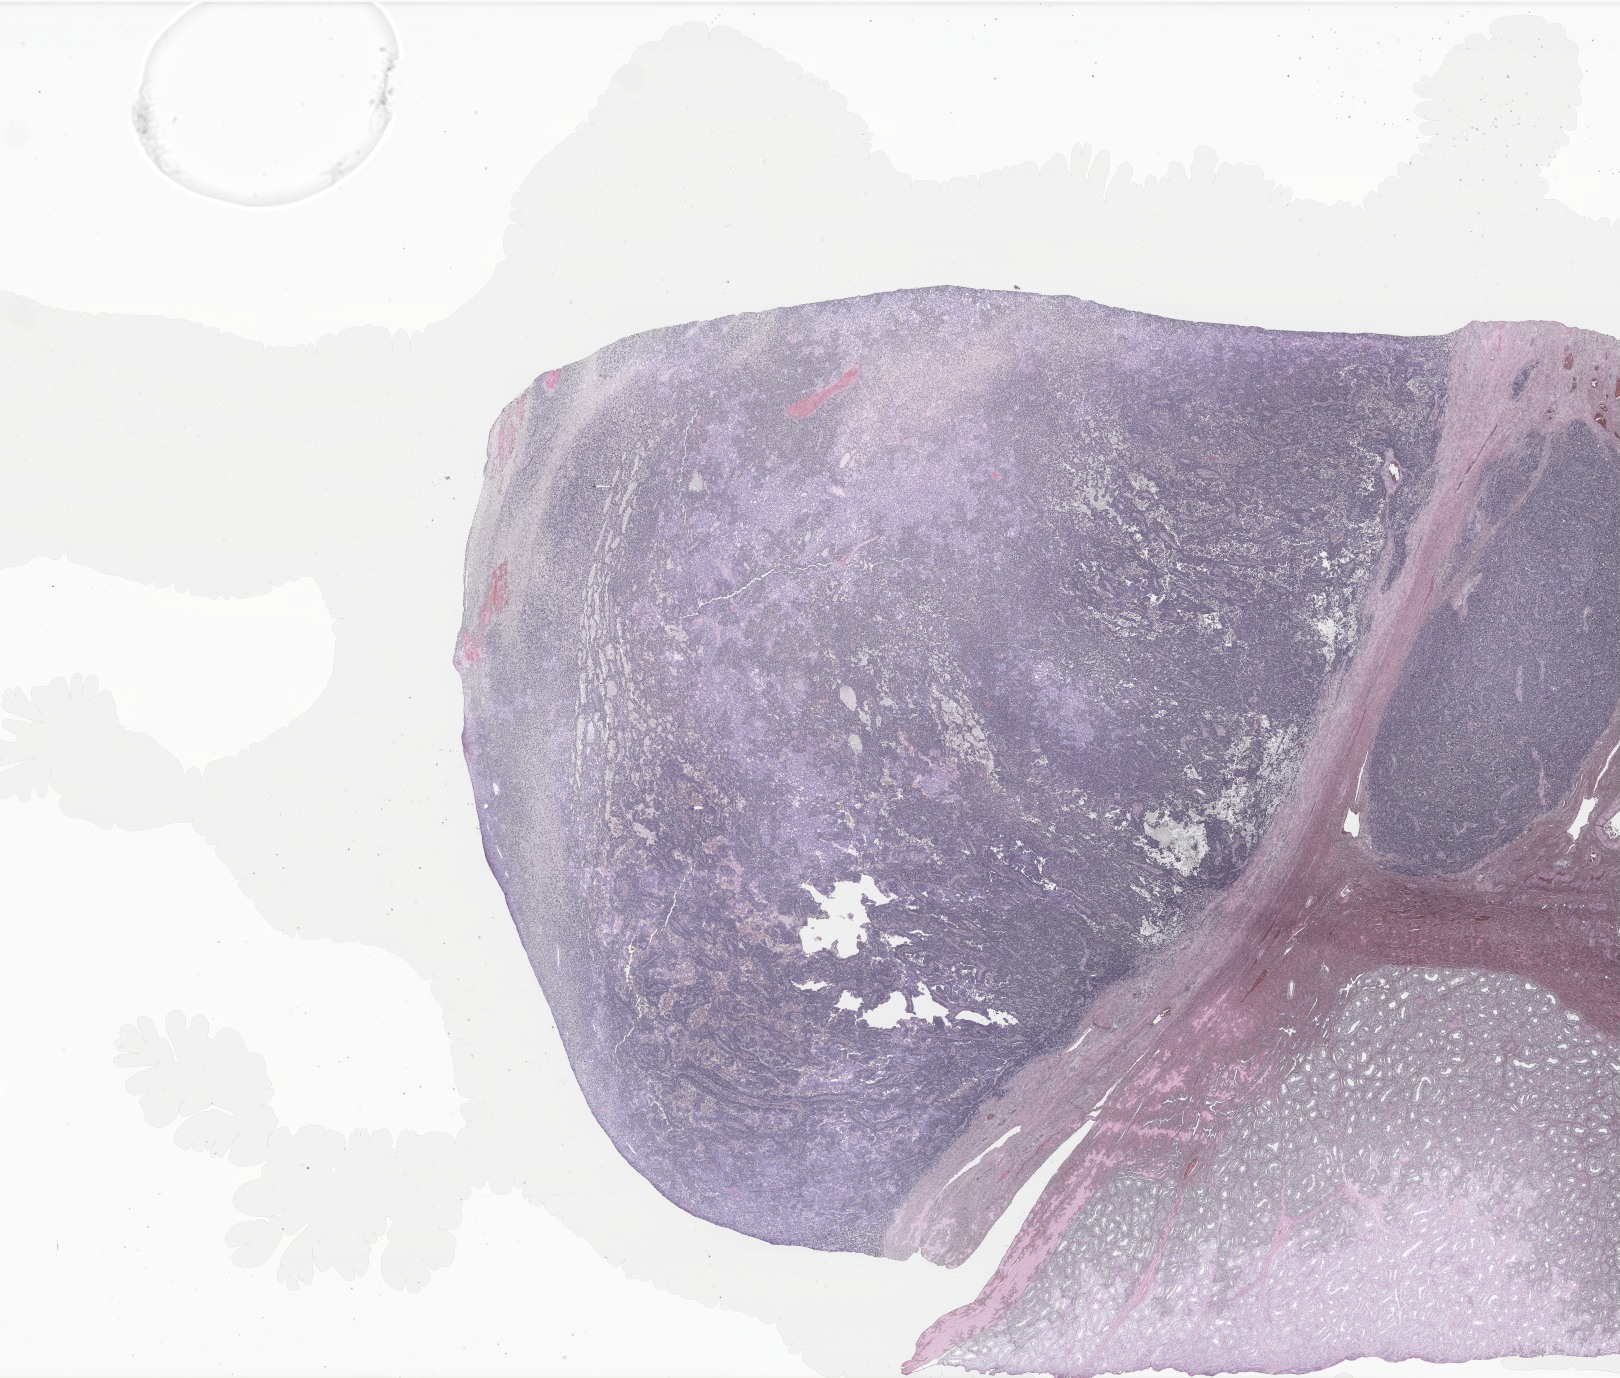
Digitized haematoxylin and eosin-stained section of tumor tissue from the testis, a low-resolution overview of the entire scanned area, about 27.3 x 23.2 mm. FFPE section. Male patient, age 153 months (12 years 9 months).
* diagnosis (ICD-O-3 morphology term): Alveolar rhabdomyosarcoma